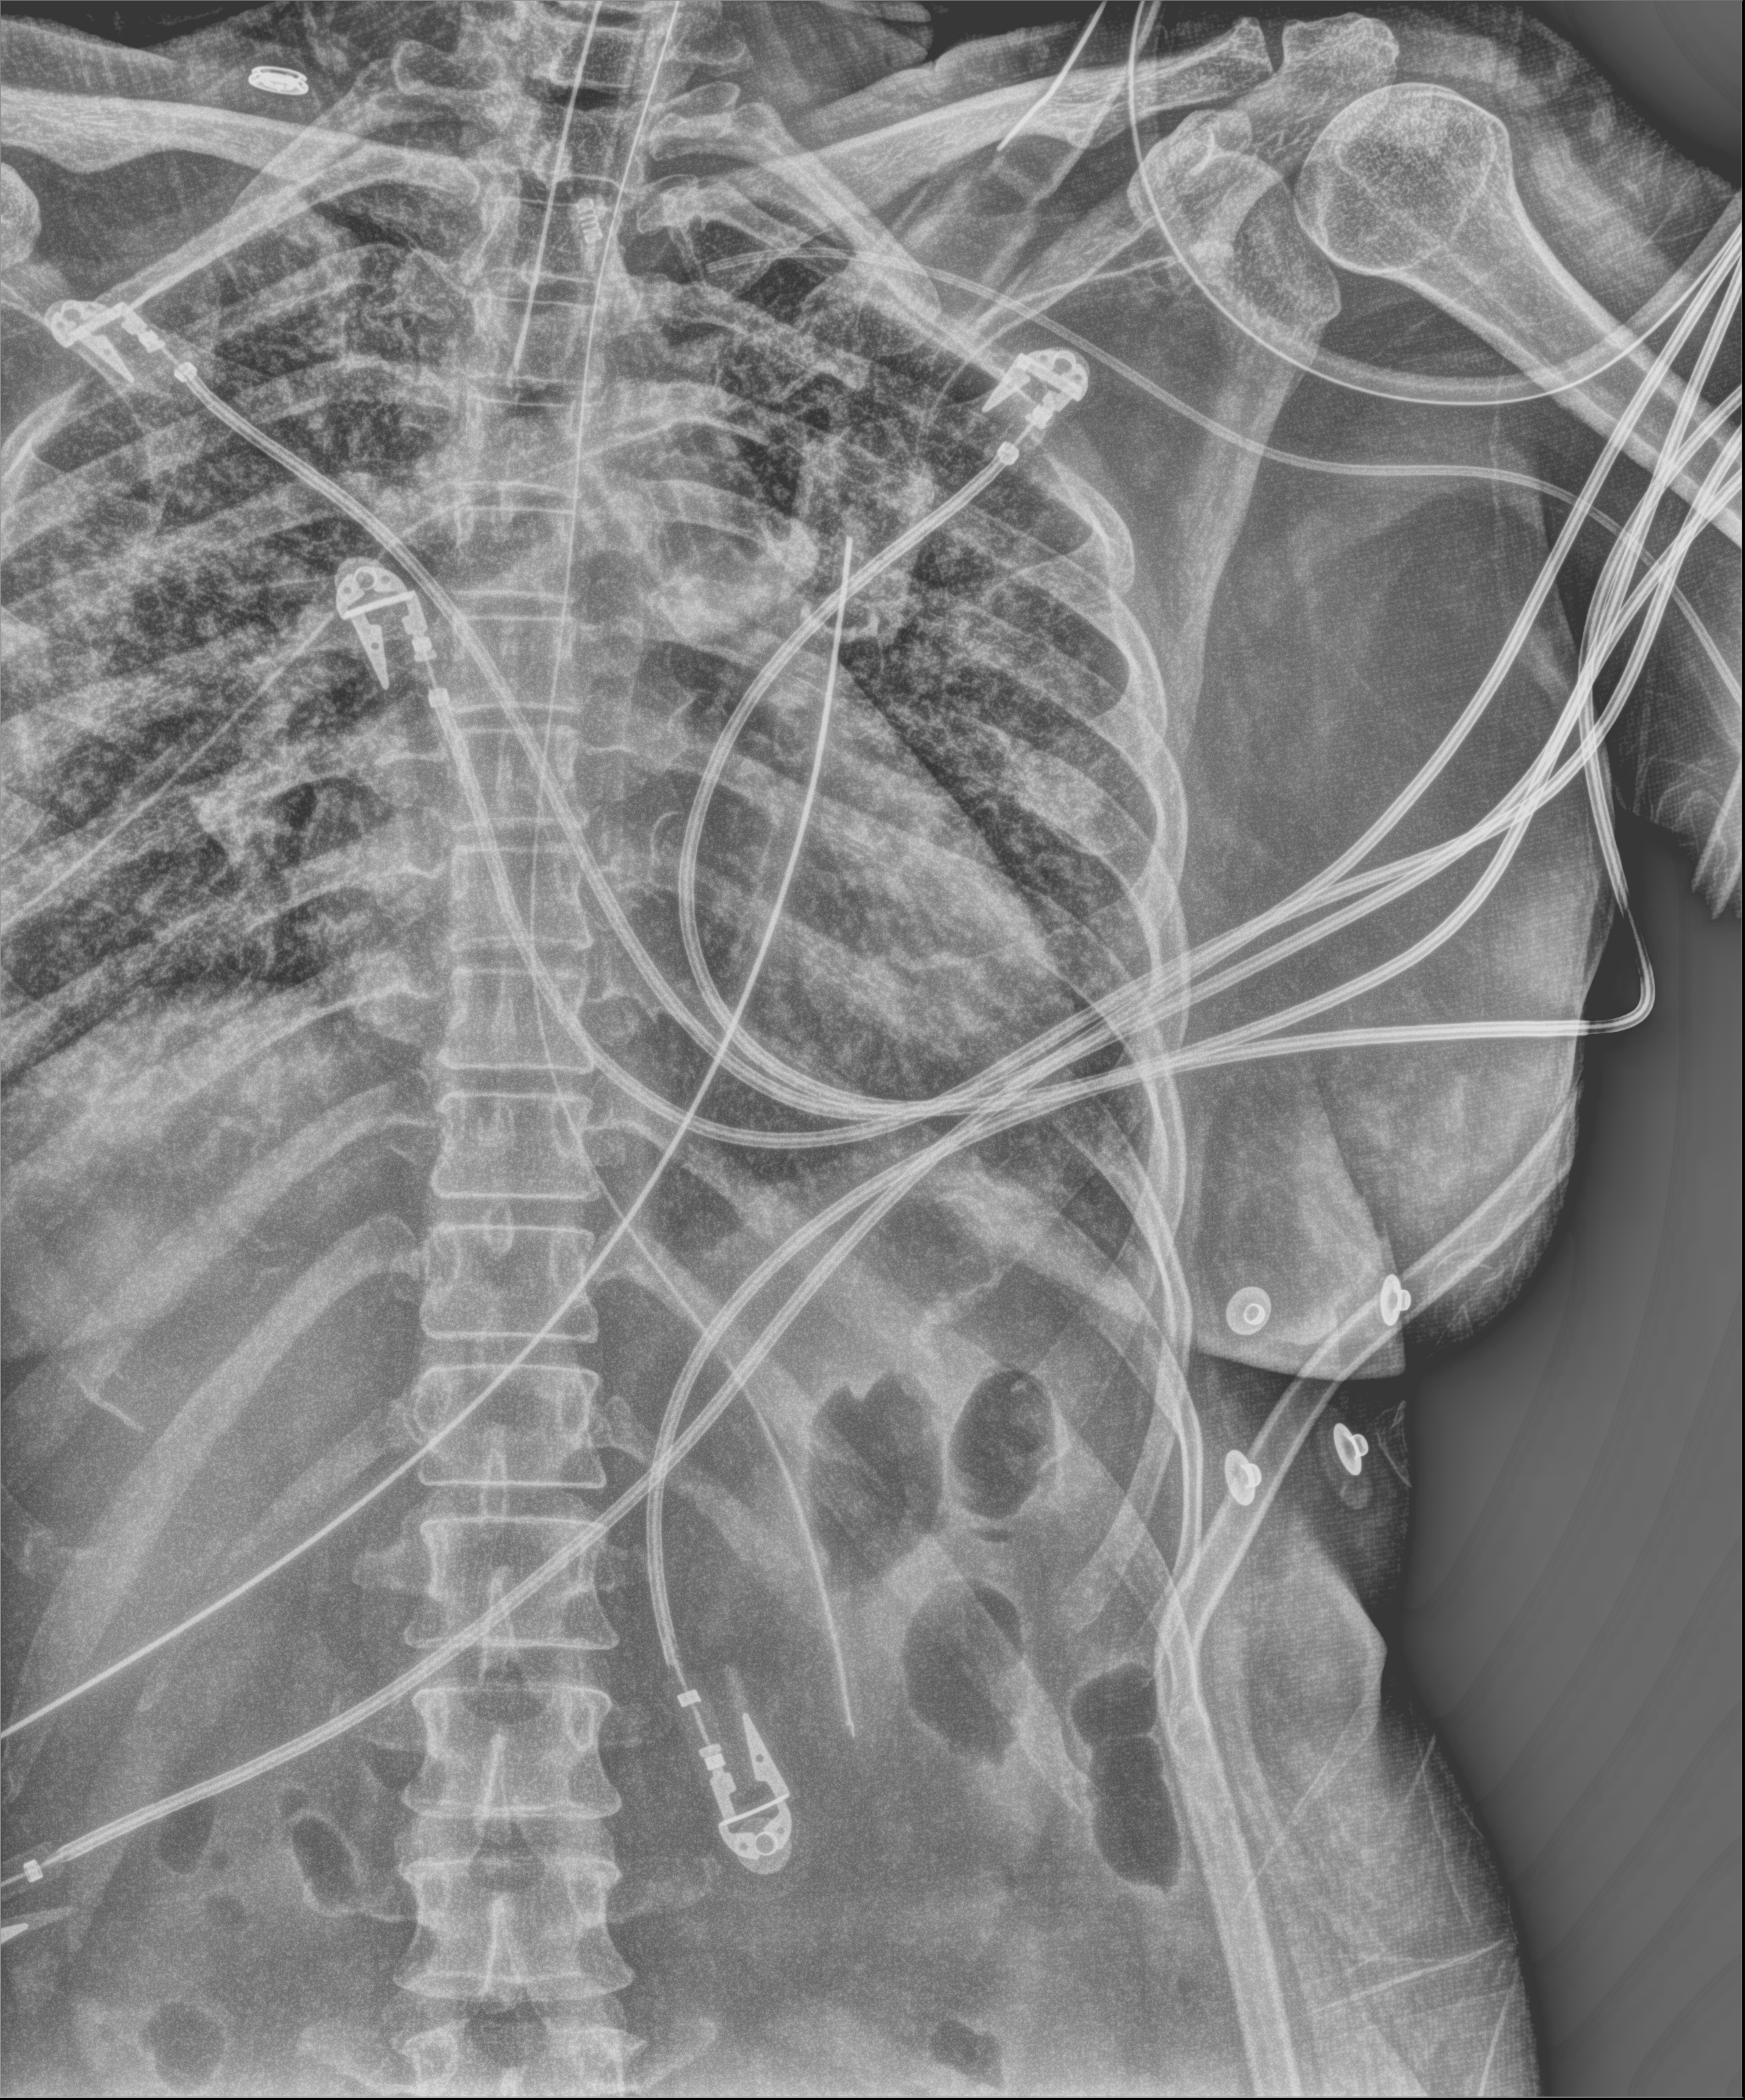
Bedside chest radiograph (digital radiography). Male patient hospitalised with COVID-19, age 18–59 years.
From the hospital-stay record, not from the radiograph (when in the stay this image was taken is not recorded): admitted to intensive care during this hospital stay: yes; mechanically ventilated during this hospital stay: yes.